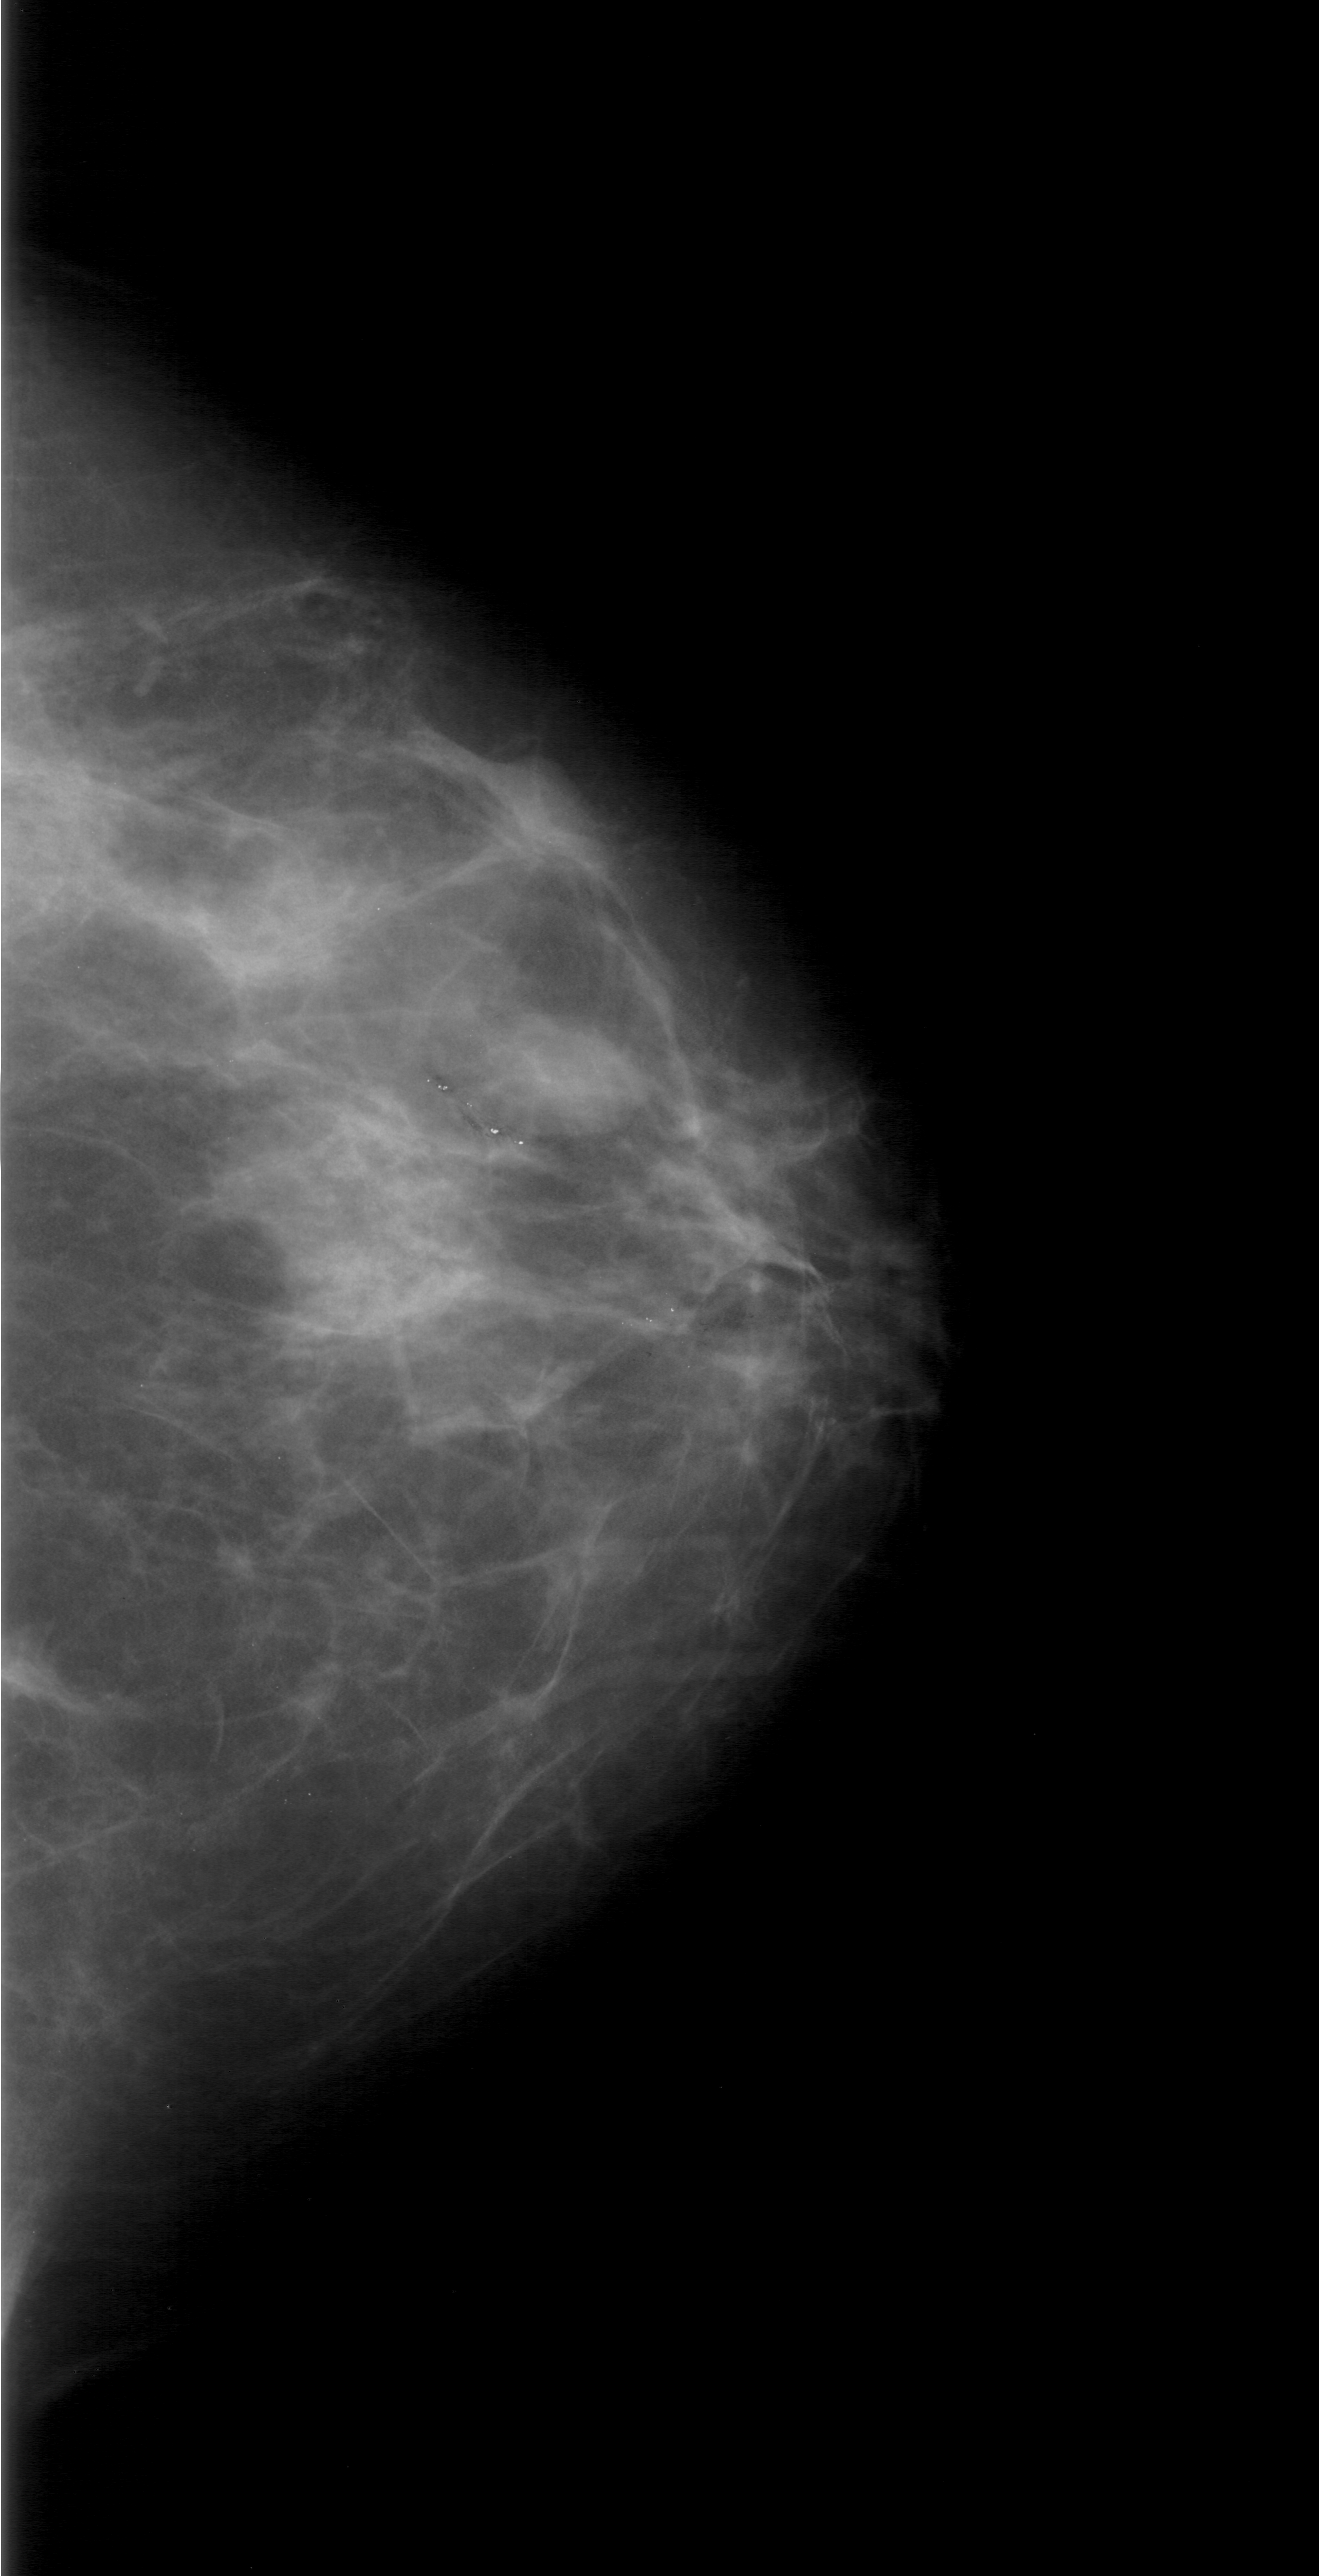
Digitized screen-film mammogram. Right breast. Craniocaudal (CC) view. BI-RADS breast density category 1 (scale 1–4). 1319 × 2576 image matrix.
Expert-marked regions of interest on this image (one box per marked abnormality):
- mass, shape oval, margins obscured; BI-RADS assessment category 3; pathology result (as recorded, not read from the image): benign: box from (x=465, y=996) to (x=679, y=1161) px